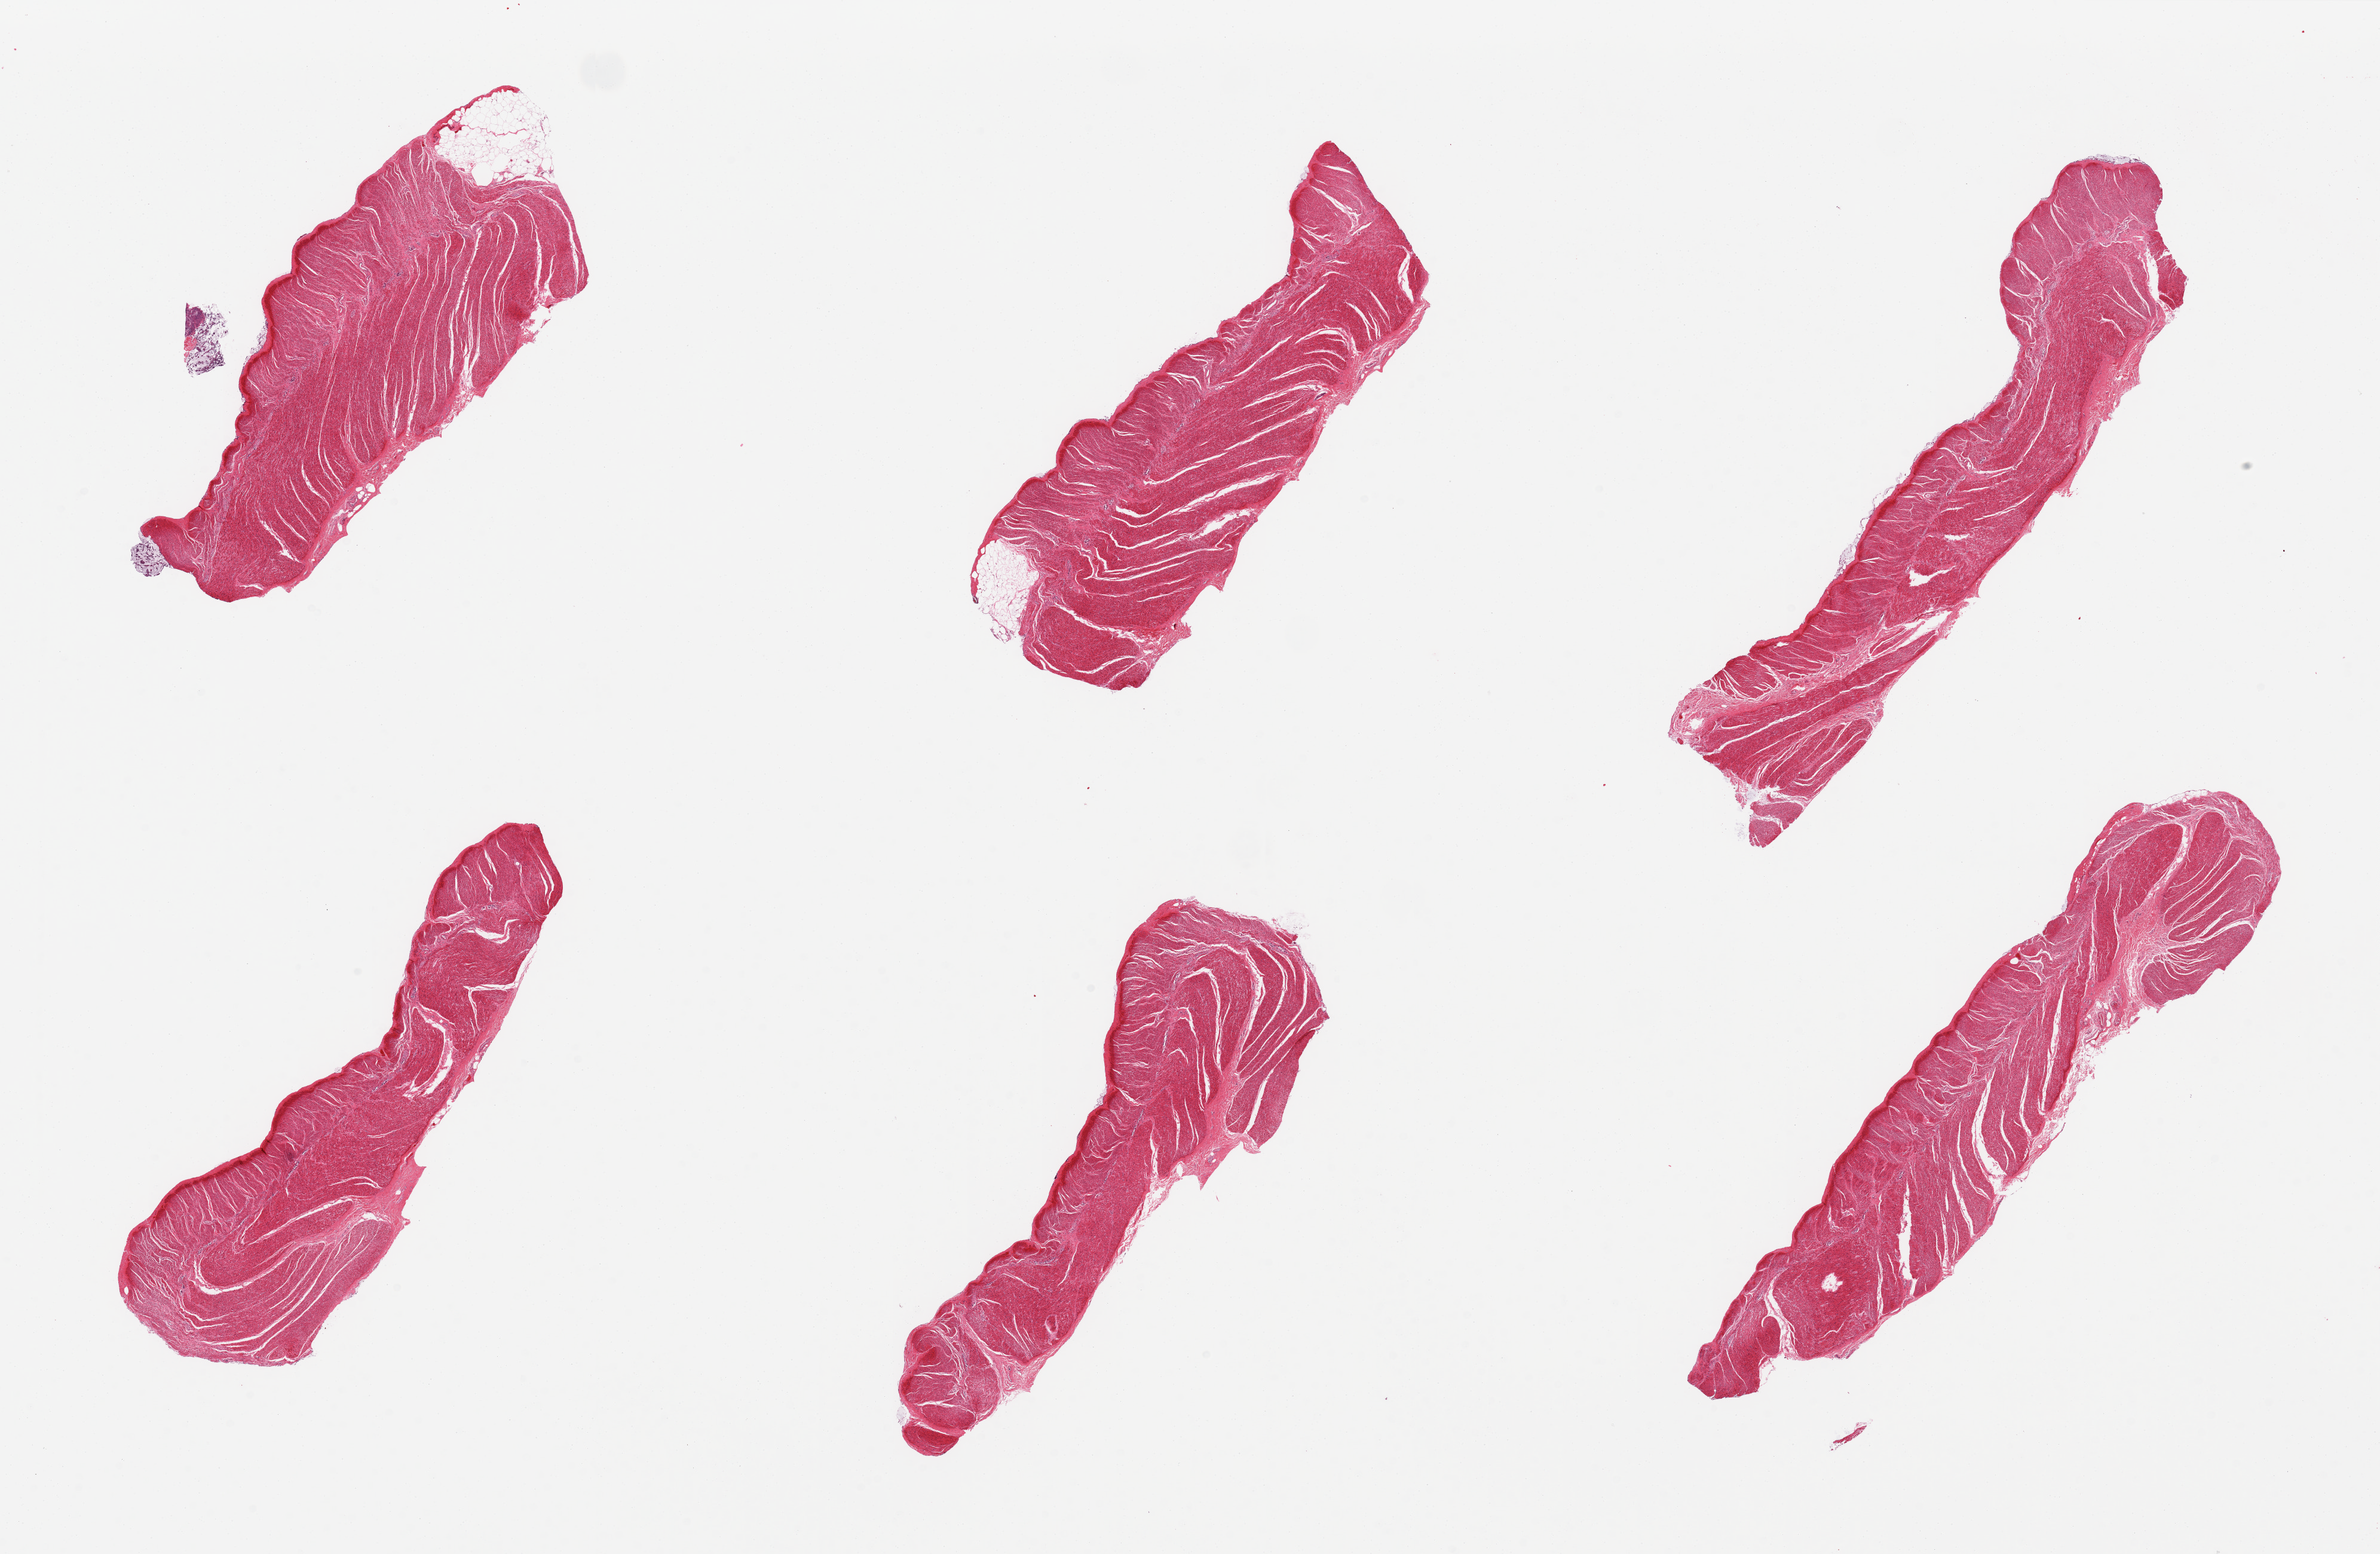
H&E whole-slide image — low-resolution overview of the scanned area, about 31.5 x 20.6 mm; PAXgene-fixed paraffin-embedded (PFPE) section; section of sigmoid colon (target tissue); tissue donor sample. Donor sex: male.
• review note (as recorded): 6 pieces, well trimmed, but with detached foci of mucin/cellular debris